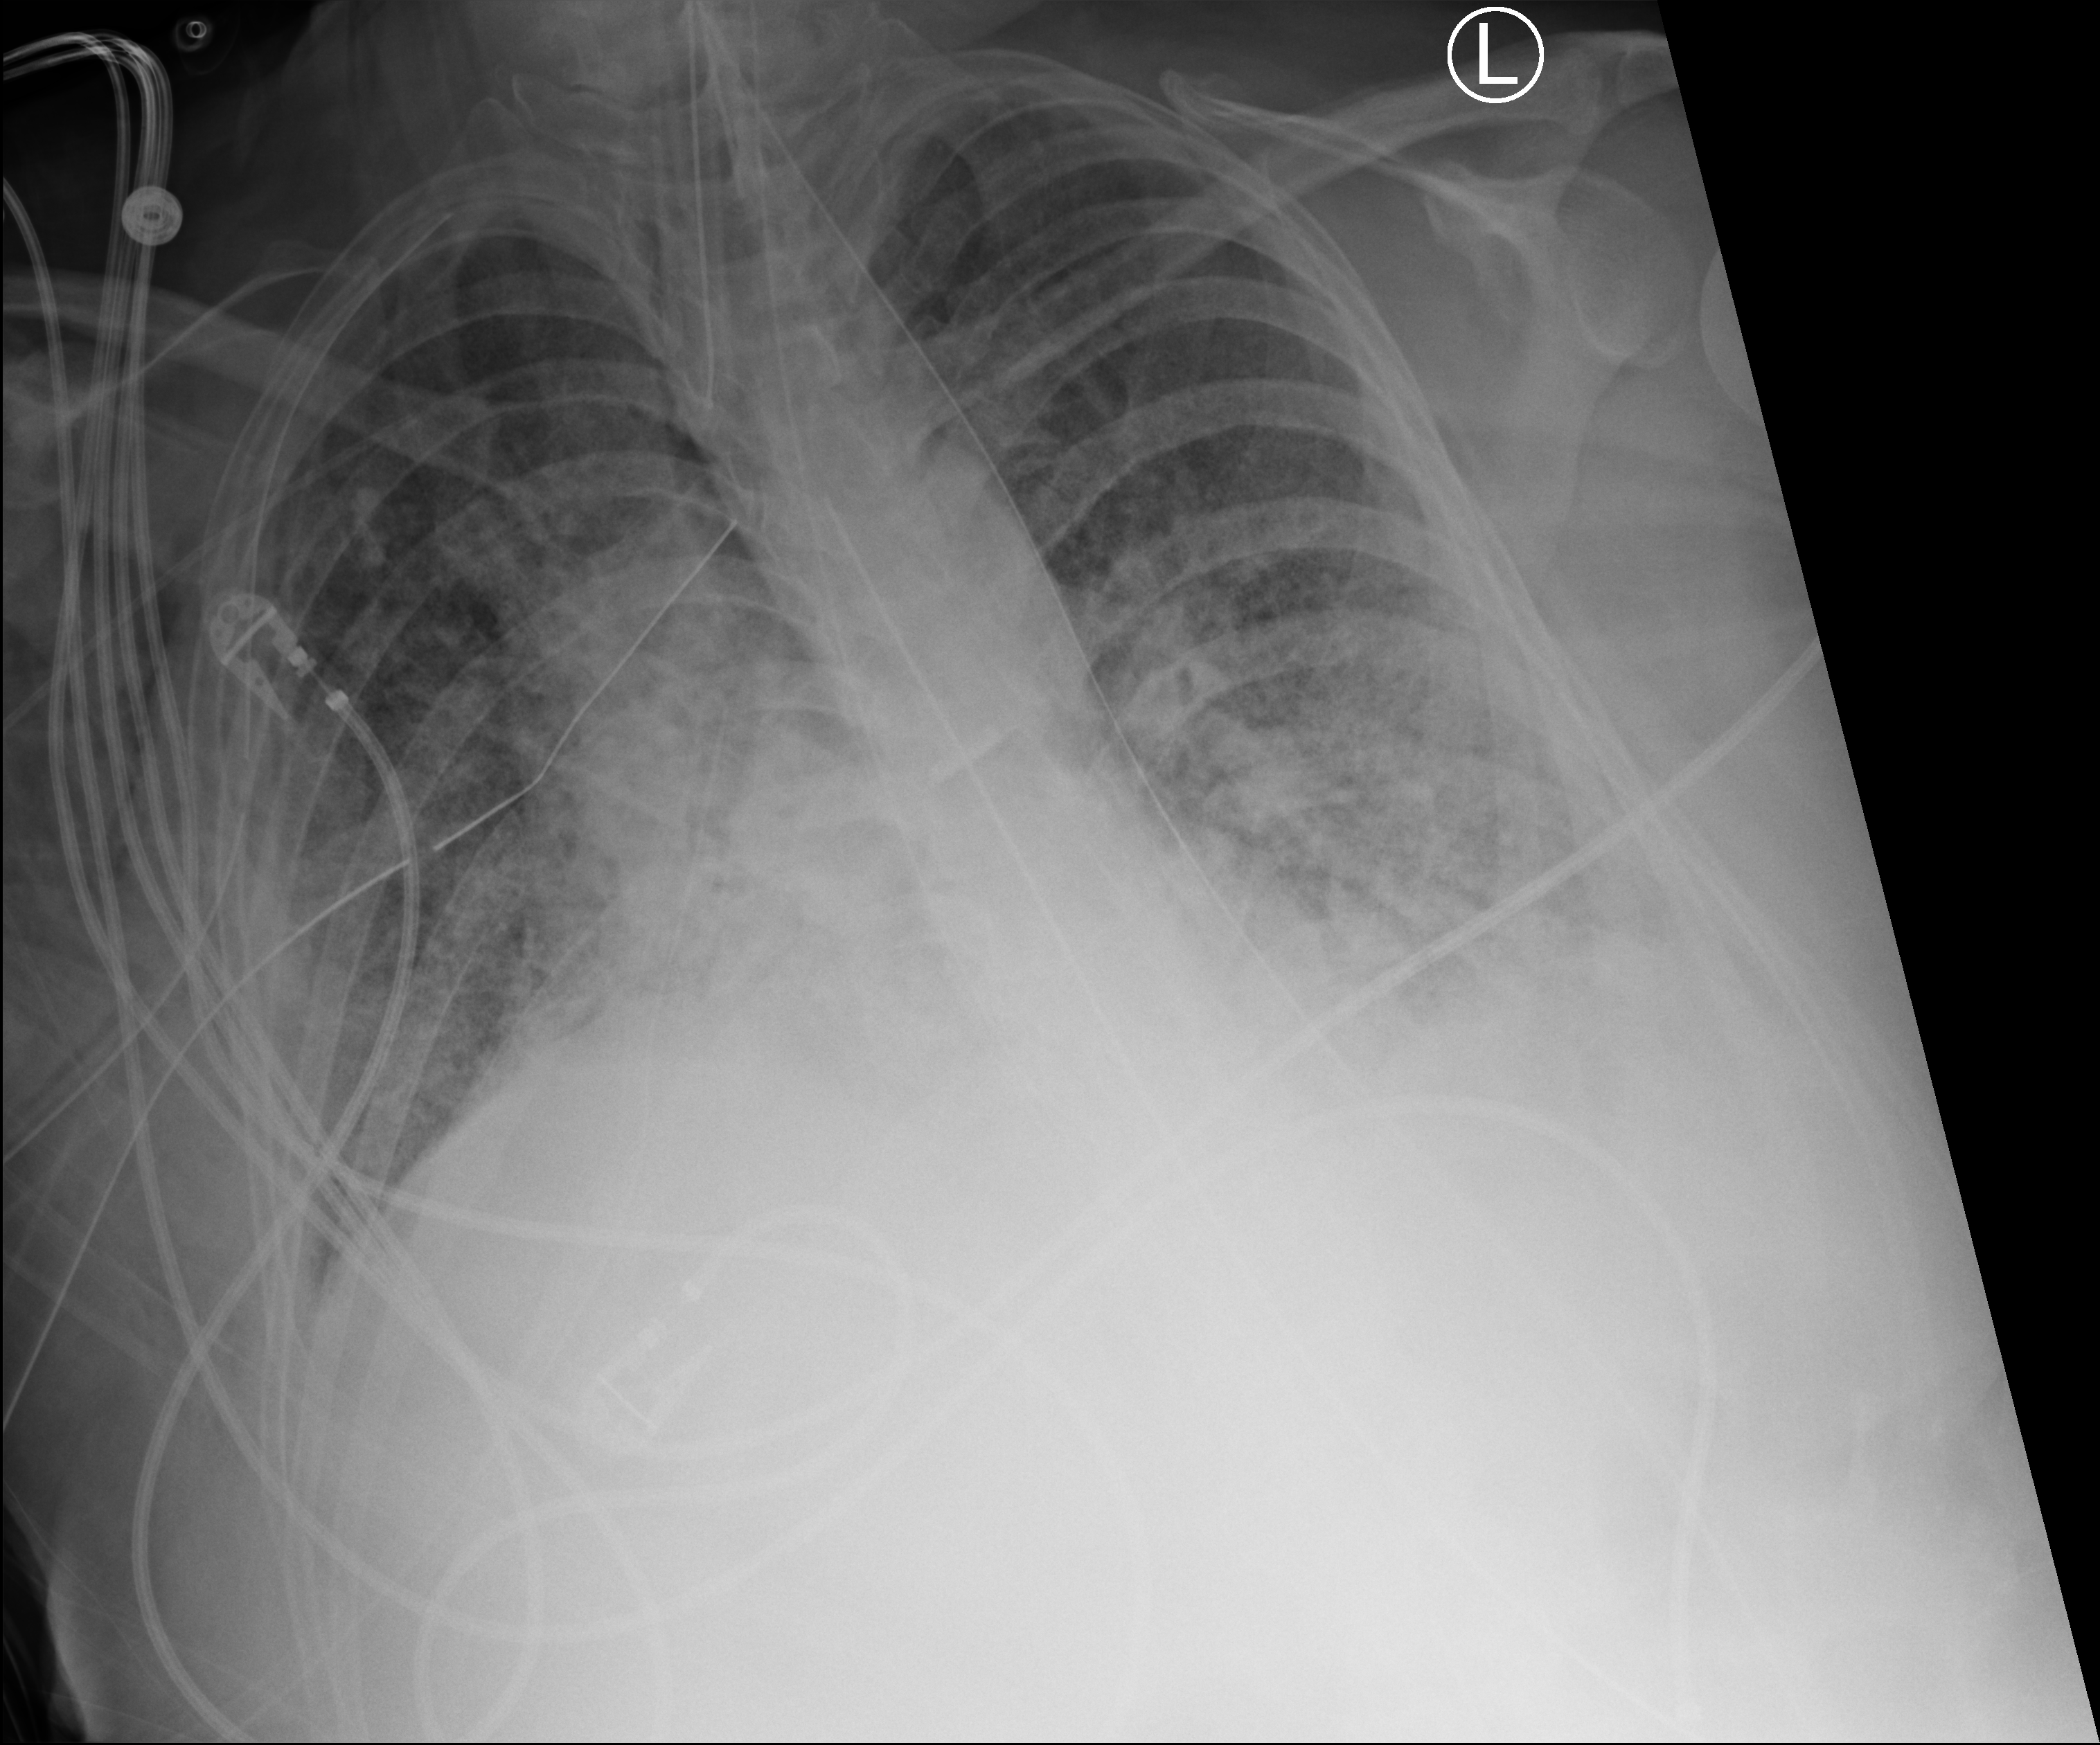
Portable chest radiograph; anteroposterior (AP) projection. Patient hospitalised with COVID-19, aged 18–59 years.
Admission-level facts for this patient (not findings on this image; timing relative to this image not recorded): mechanically ventilated during this hospital stay: yes.